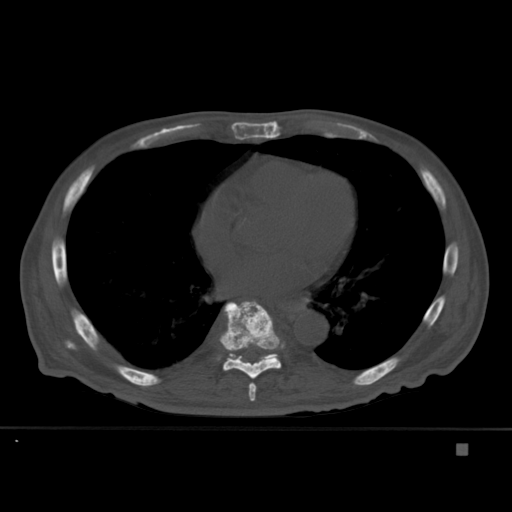
CT including the spine, one axial slice. Position 262 of 451 along the scan axis. Bone window (W 1800 / L 400 HU). 512 × 512 image matrix, field of view 378 × 378 mm. Patient: male, 75 years. Case-level facts recorded for this patient, not image findings: primary cancer: prostate.
Outlined on this slice (semi-automatic segmentation, software-assisted and operator-edited):
- T7 vertebra: bounding box [x1, y1, x2, y2] px = [249, 382, 257, 401]
- T8 vertebra: [219, 301, 282, 379]
- T9 vertebra: [224, 353, 278, 363]